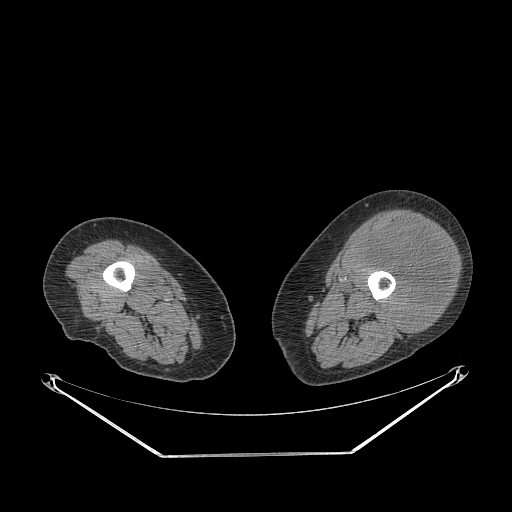
CT of an extremity soft-tissue mass (from a PET/CT study), one axial slice. Reconstruction kernel STANDARD. Soft-tissue window (W 400 / L 40 HU). 3.75 mm slice thickness. 512 × 512 image matrix, field of view 500 × 500 mm. Female patient. Case-level facts recorded for this patient, not image findings: histological type: undifferentiated – high grade; grade: high; site of the primary tumour: left thigh.
Outlined on this slice (expert contour drawn on MRI and transferred to this co-registered scan by the dataset authors):
- gross tumour volume including surrounding oedema: box from (x=358, y=219) to (x=453, y=330) px
- gross tumour volume (mass): (x=359, y=219)–(x=451, y=330)